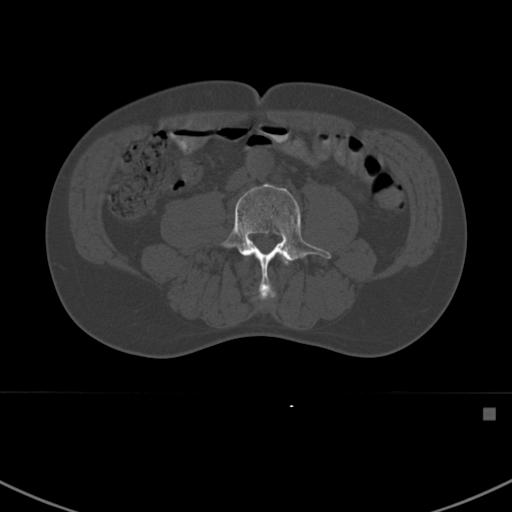
CT including the spine, one axial slice; slice 244 of 412 in the series (ordered by position); 120 kVp; bone window (W 1800 / L 400 HU); 1.5 mm slice thickness; 512 × 512 image matrix, field of view 358 × 358 mm. Patient: male, 59 years. From the clinical record (not read from this slice): primary cancer: prostate.
Annotated regions visible in this slice (semi-automatically segmented with operator editing):
- L3 vertebra: bounding box (x1, y1, x2, y2) in pixels: (258, 256, 290, 301)
- L4 vertebra: (218, 183, 331, 296)